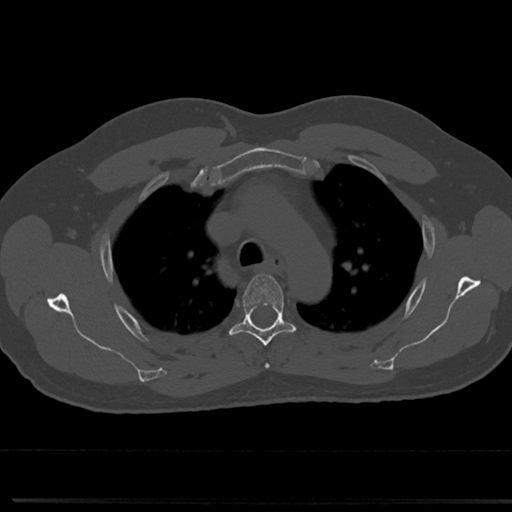
CT including the spine, one axial slice. Position 549 of 817 along the scan axis. Reconstruction kernel Br40s/3. Bone window (W 1800 / L 400 HU). 0.5 mm slice thickness. 512 × 512 image matrix, field of view 355 × 355 mm. Patient: male, 61 years. From the clinical record (not read from this slice): primary cancer: prostate.
Annotated regions visible in this slice (semi-automatically segmented with operator editing):
- T3 vertebra: box from (x=264, y=363) to (x=269, y=368) px
- T4 vertebra: (x=223, y=273)–(x=300, y=345)